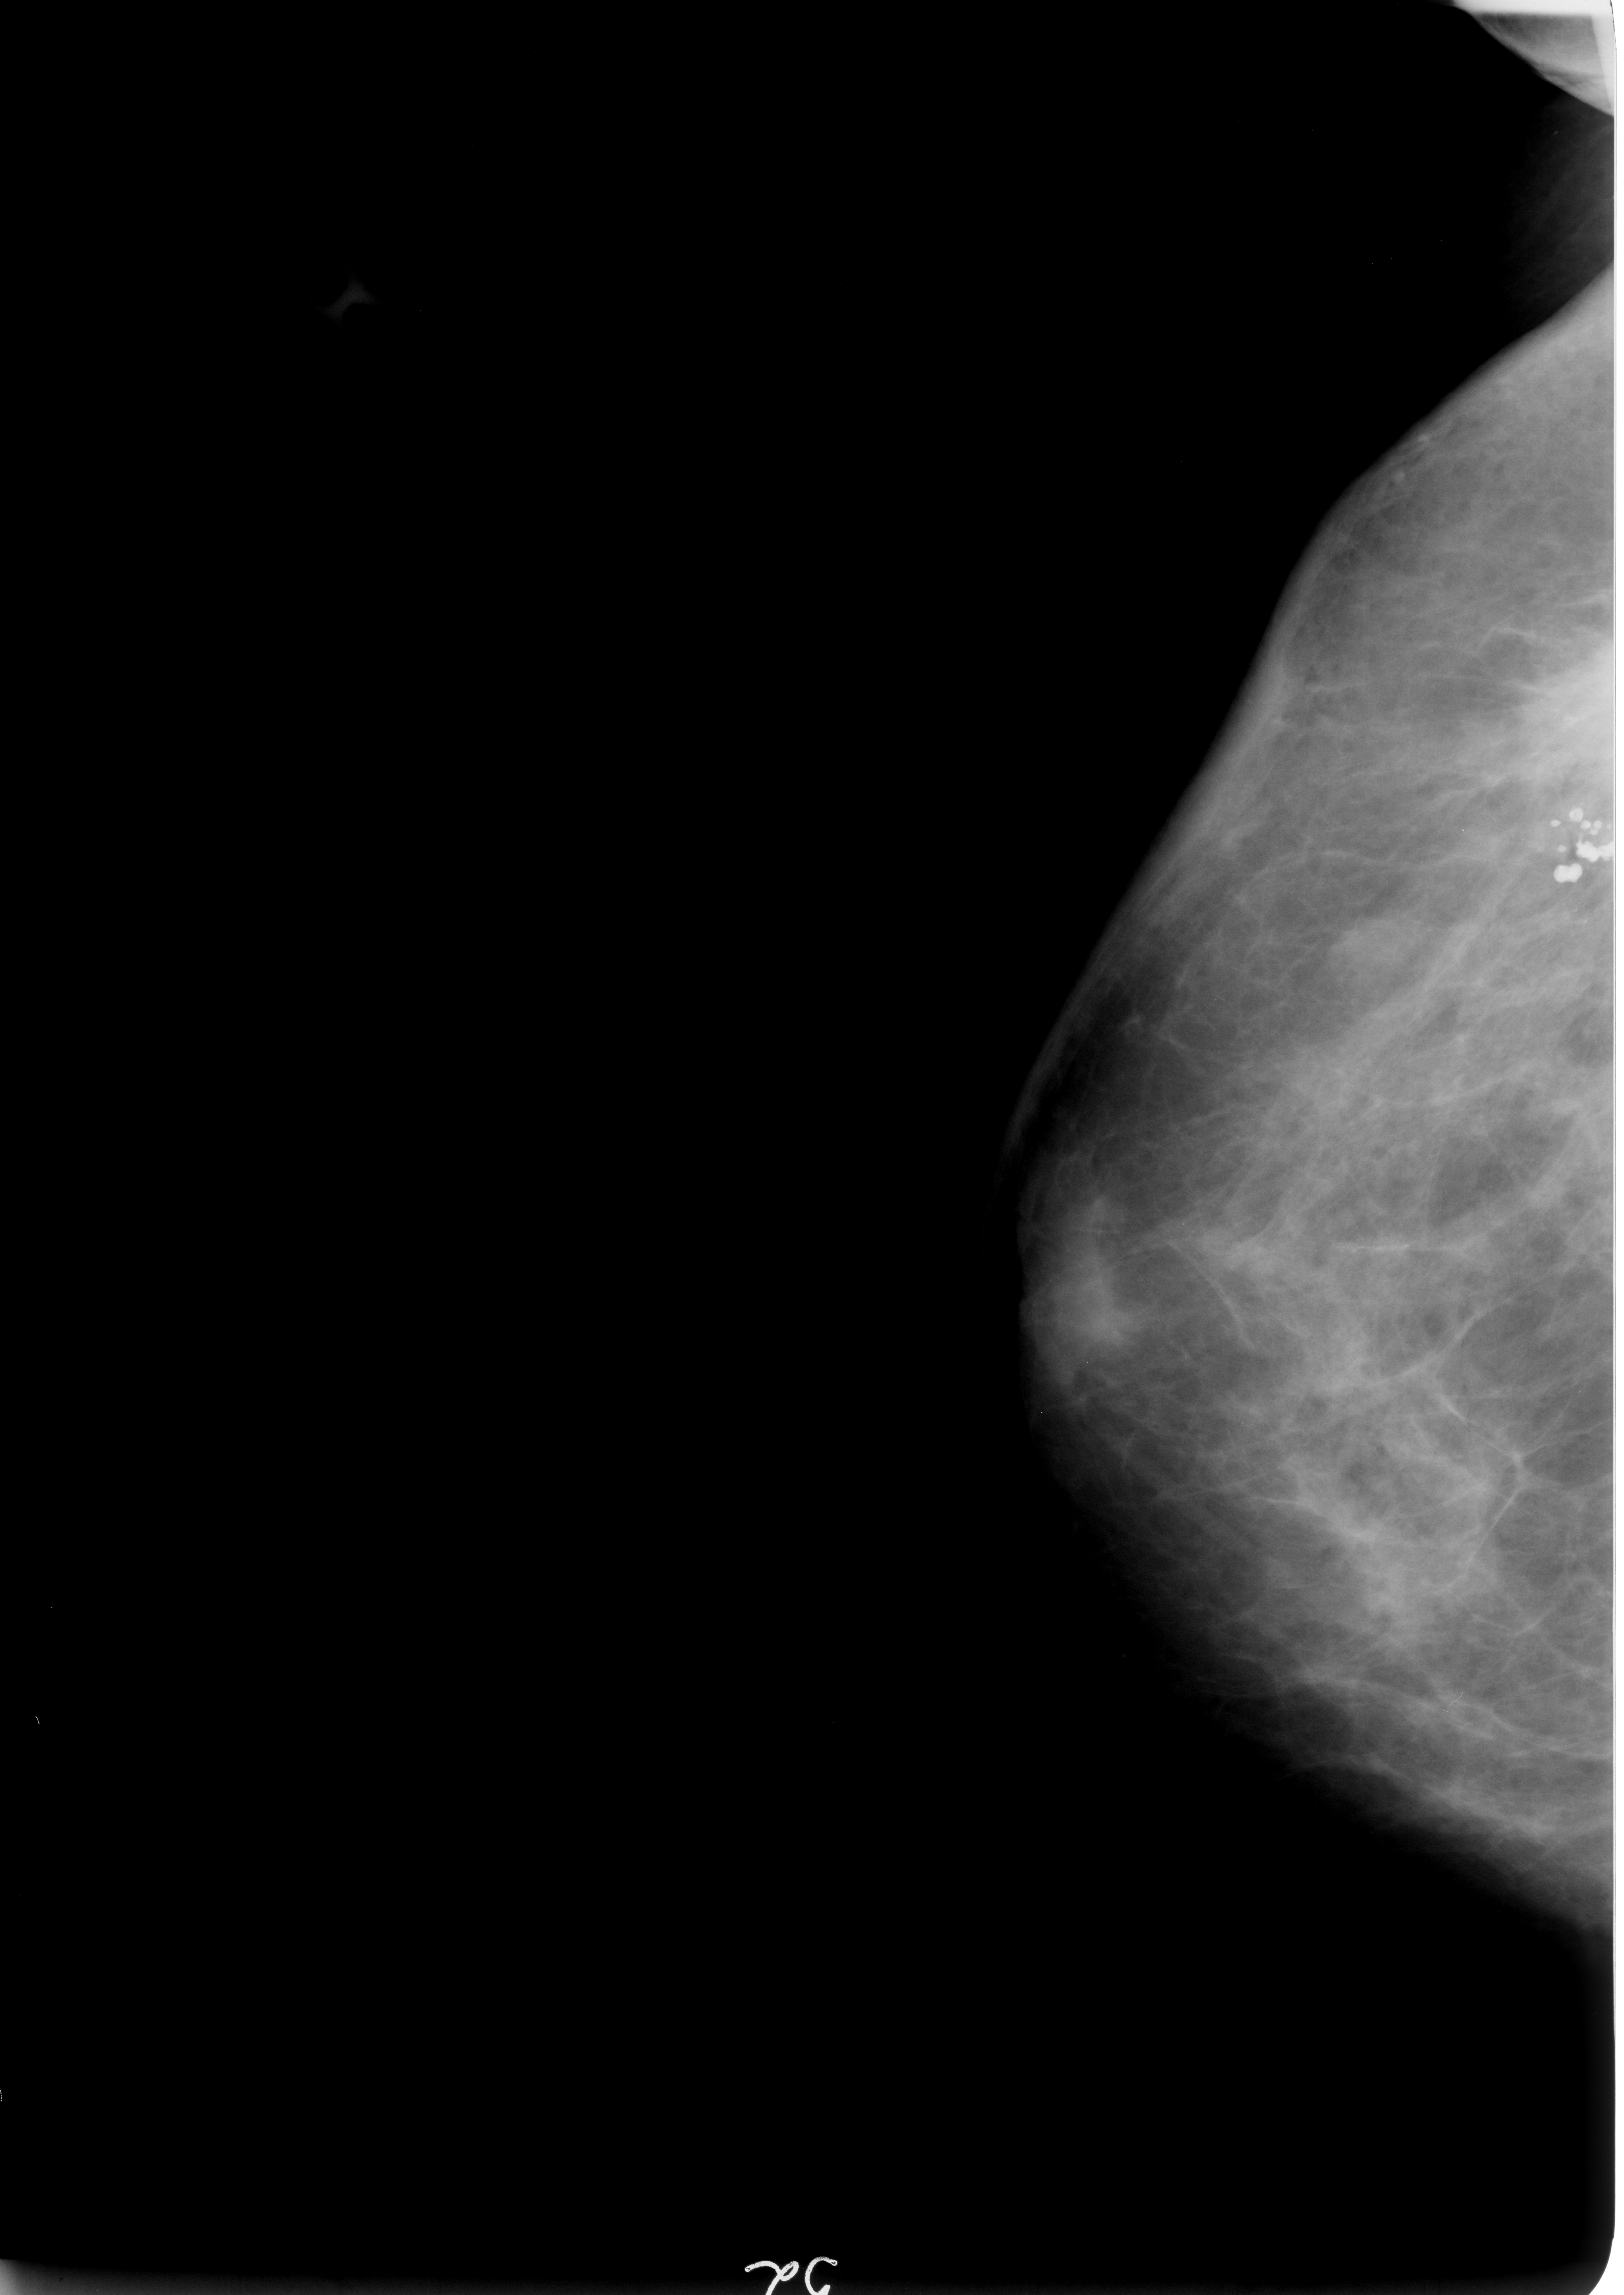
Digitized screen-film mammogram; right breast; CC view; BI-RADS breast density category 2 (scale 1–4).
Marked findings (only marked abnormalities are described; nothing is implied about the rest of the image): Finding 1 of 2: mass, shape irregular / architectural distortion, margins ill defined / spiculated; BI-RADS assessment category 5; subtlety rating 5 on a 1 (subtle) to 5 (obvious) scale; pathology result (as recorded, not read from the image): malignant. Finding 2 of 2: mass, shape irregular / architectural distortion, margins ill defined / spiculated; BI-RADS assessment category 5; pathology (as recorded): malignant.